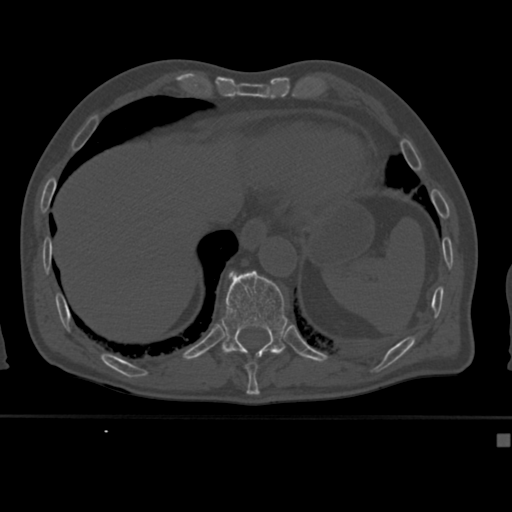
CT including the spine, one axial slice. Position 216 of 430 along the scan axis. Bone window (W 1800 / L 400 HU). 512 × 512 image matrix, field of view 337 × 337 mm. Male patient, age 64 years. Case-level facts recorded for this patient, not image findings: primary cancer: uterus.
Annotated regions visible in this slice (semi-automatically segmented with operator editing):
- T10 vertebra: box from (x=245, y=361) to (x=258, y=382) px
- T11 vertebra: (x=221, y=270)–(x=288, y=358)